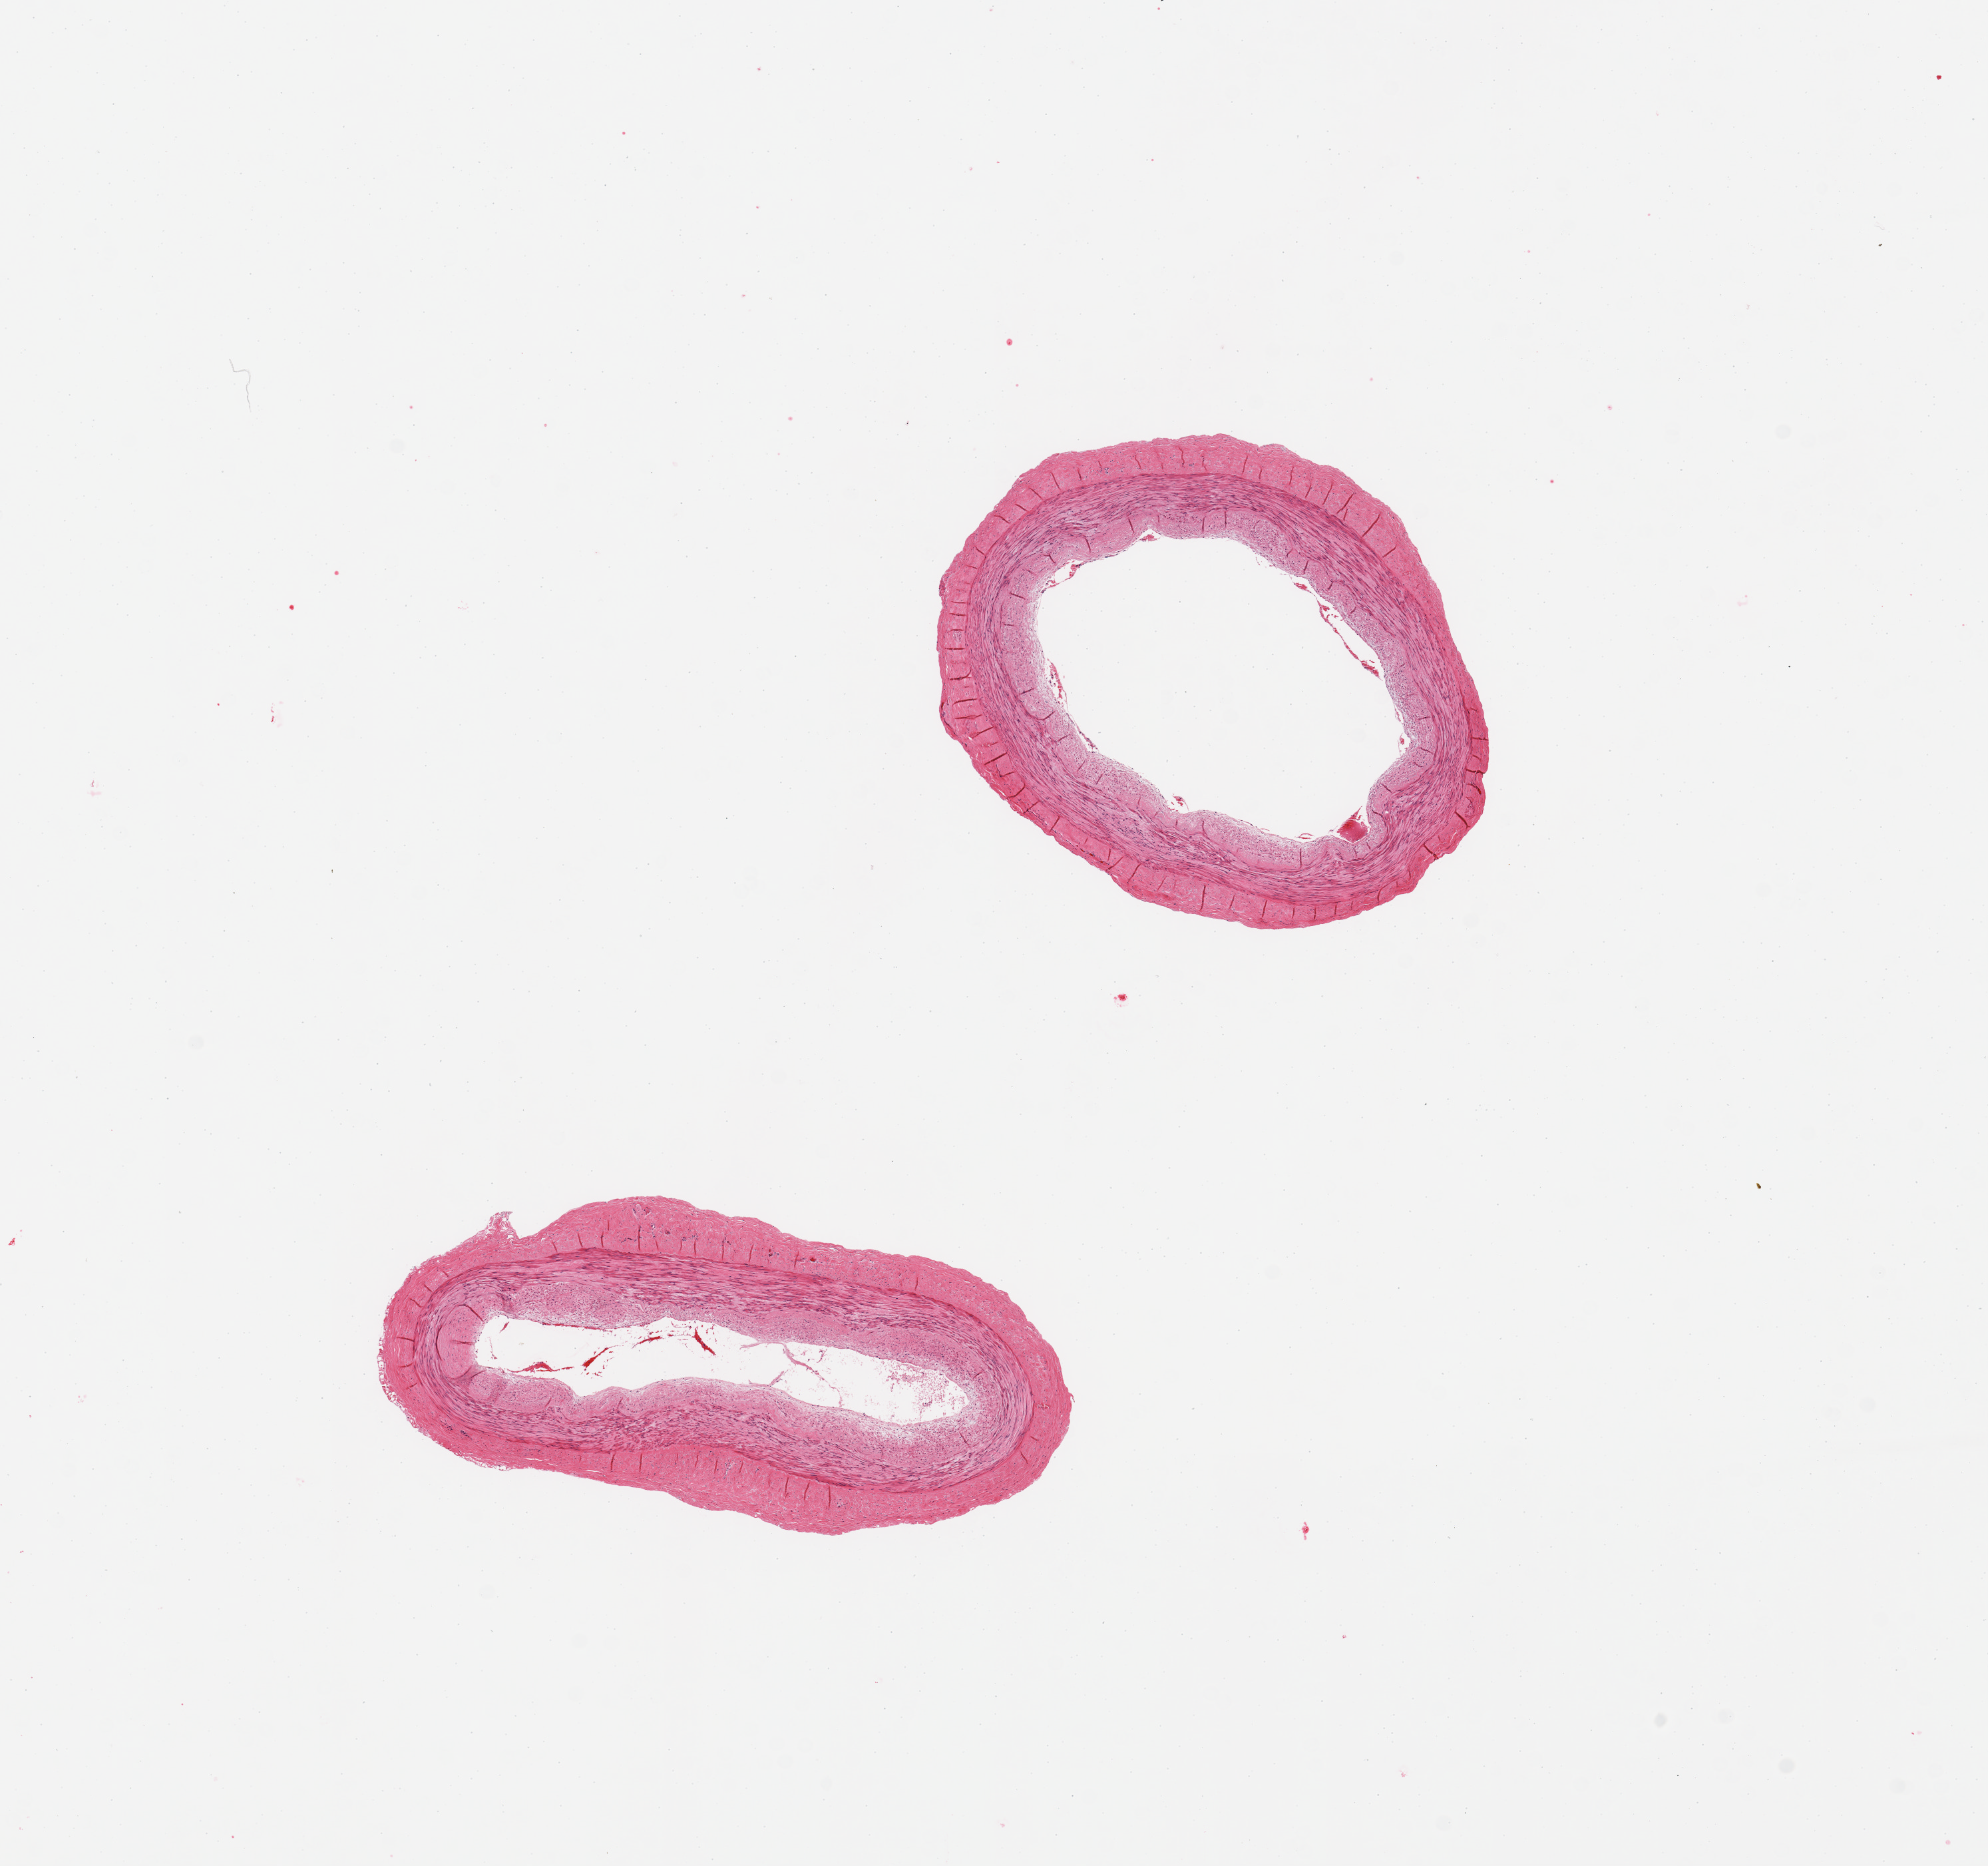
Whole-slide image, haematoxylin and eosin stain, brightfield, a low-resolution overview of the entire scanned area, about 11.8 x 11.1 mm; PAXgene-fixed paraffin-embedded (PFPE) section; target tissue: tibial artery; tissue donor sample. Male donor.
Review note (as recorded): 2 pieces; well trimmed; intimal thickening/mild plaque.